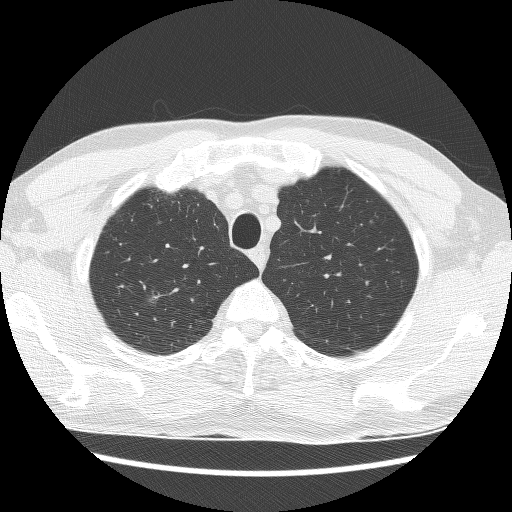
Low-dose screening chest CT, one axial slice; slice 131 of 157 in the series (ordered by position); 120 kVp; lung window (W 1500 / L -600 HU); 2.5 mm slice thickness; 512 × 512 image matrix, field of view 340 × 340 mm.
Annotated regions visible in this slice (outlined manually by an expert reader):
- lesion 1 (tumor, upper lobe of right lung): bounding box [x1, y1, x2, y2] px = [149, 297, 157, 309]